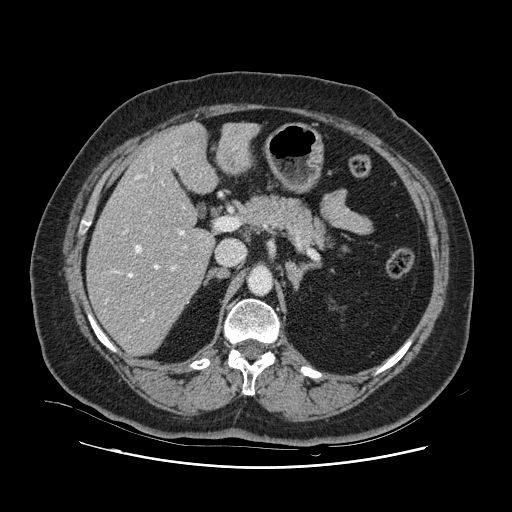
Contrast-enhanced abdominal CT, one axial slice. Slice 60 of 132 in the series (ordered by position). Soft-tissue window (W 400 / L 40 HU). 512 × 512 image matrix. Female patient, age 73 years. Case-level facts recorded for this patient, not image findings: diagnosis: colorectal cancer liver metastases, imaged before liver resection; multiple liver metastases: no; largest metastasis: 7 cm.
Annotated regions visible in this slice (outlined manually by an expert reader):
- hepatic veins: bounding box (x1, y1, x2, y2) in pixels: (111, 156, 185, 322)
- liver: (88, 124, 255, 355)
- planned liver remnant (the part of the liver to remain after resection): (88, 149, 214, 355)
- portal vein (with intrahepatic branches): (171, 217, 226, 270)